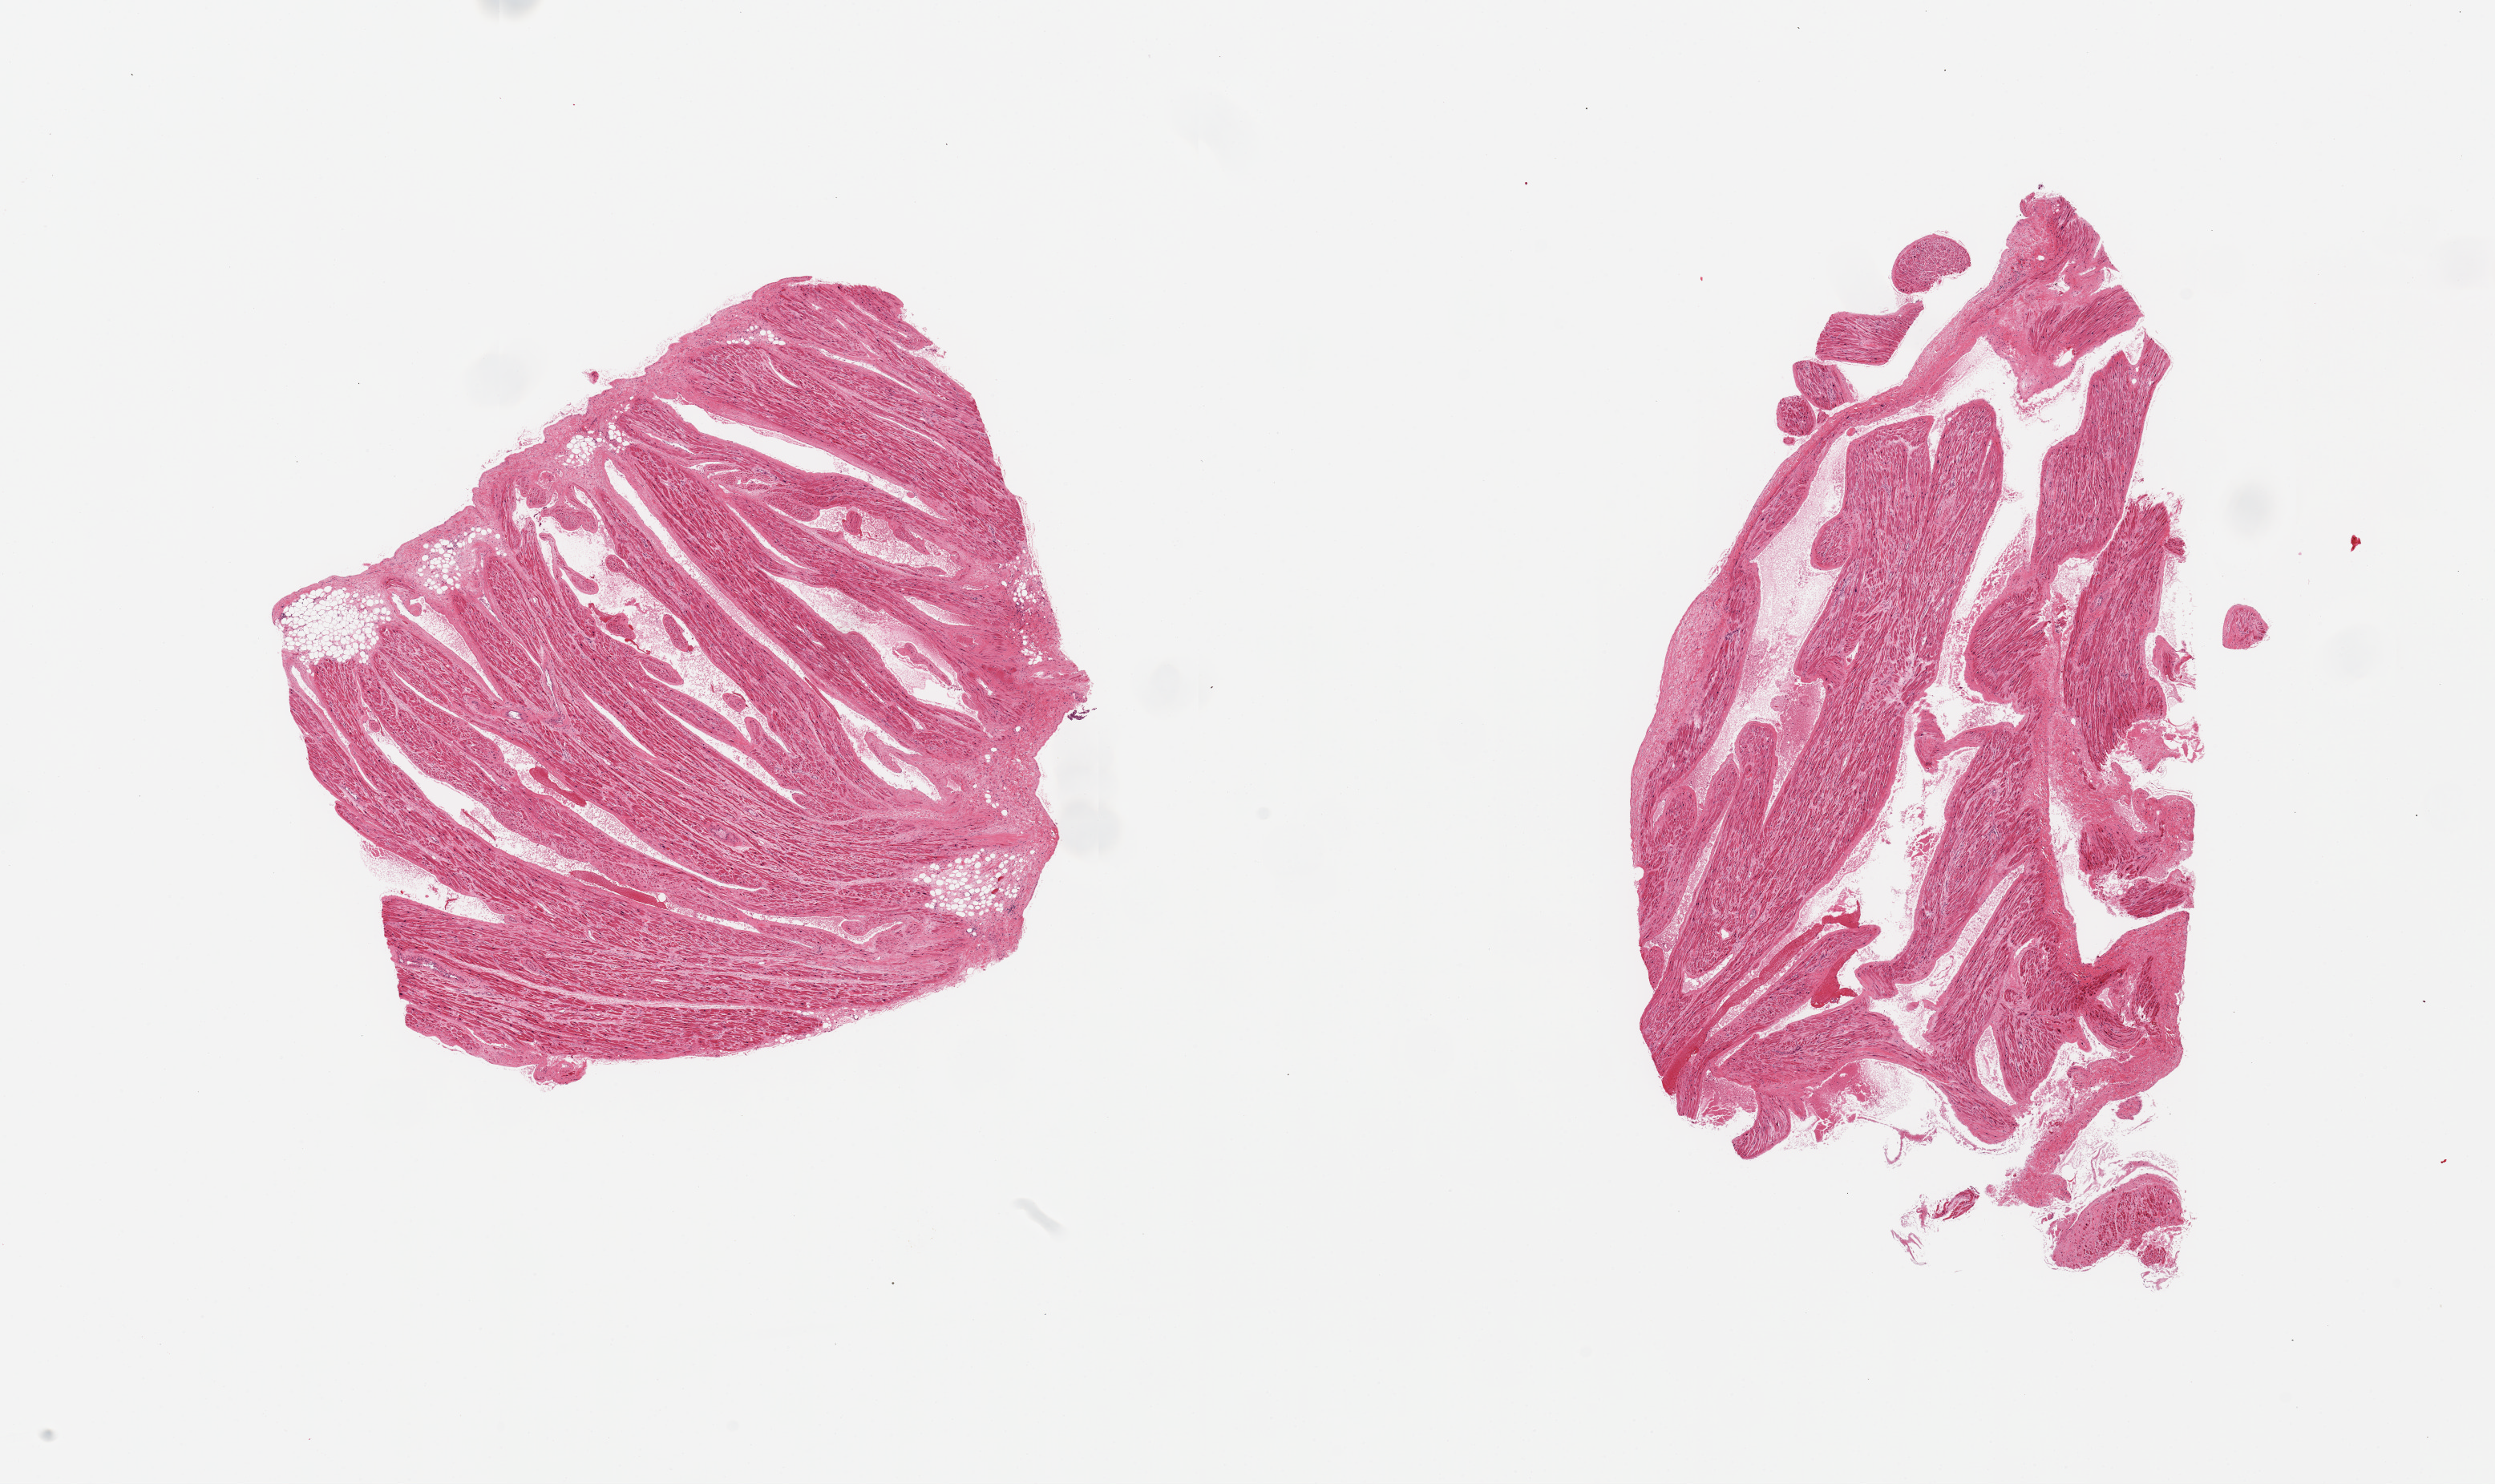
Digitized H&E-stained section, whole scanned area (about 24.6 x 14.6 mm, acquisition: 20x scan) shown as a low-resolution overview, PAXgene-fixed paraffin-embedded (PFPE) section, section of auricular appendage (target tissue), donor tissue sample. Donor: male.
Pathologist's review note for this sample: 2 pieces; hypertrophy and interstitial fibrosis, small amount of internal fat.